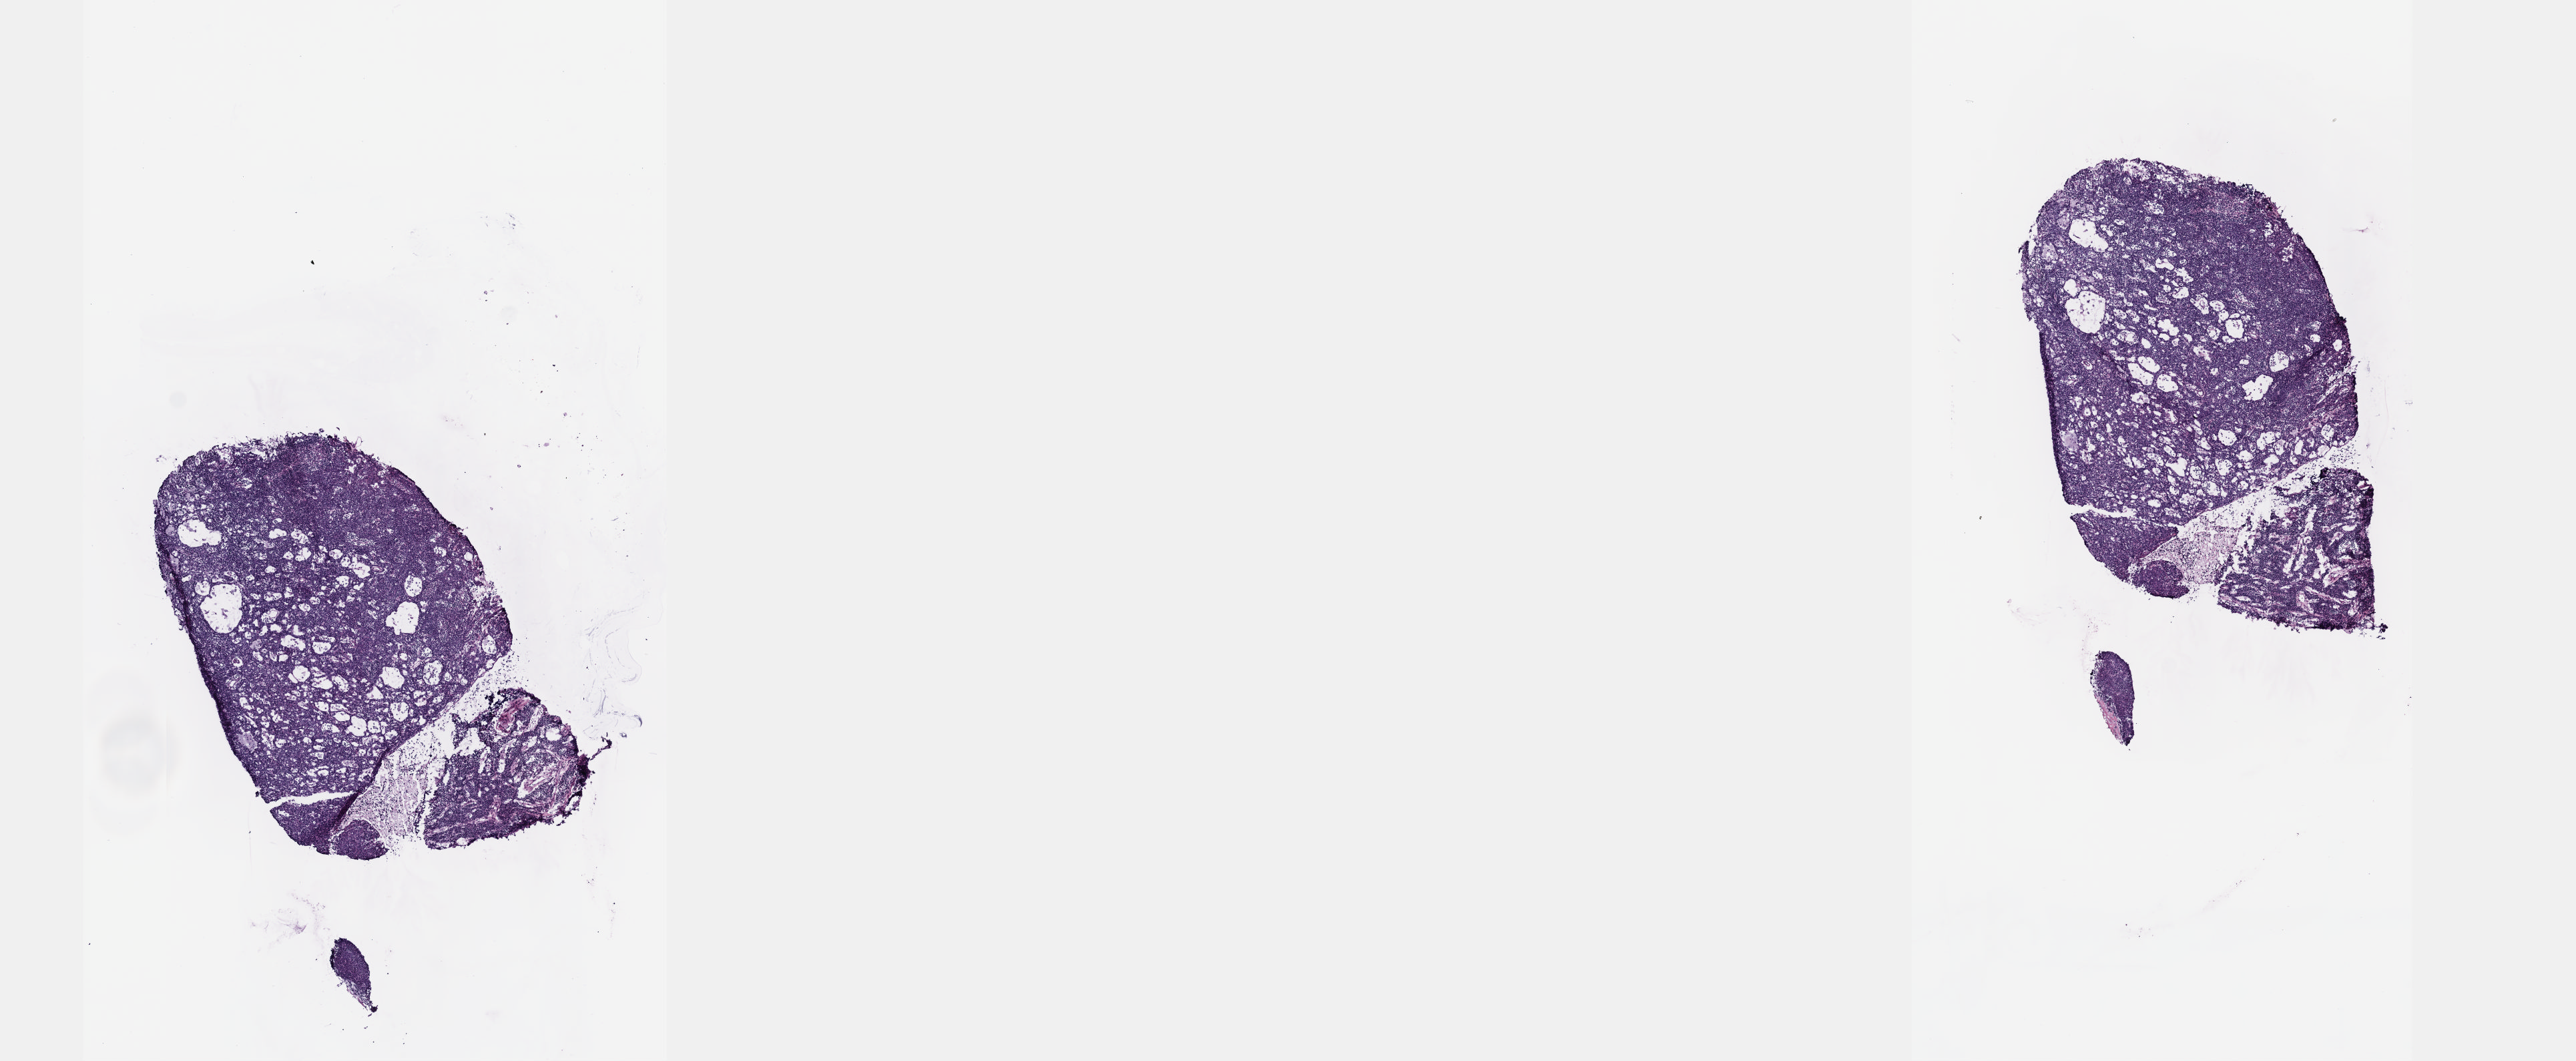
Digitized H&E-stained tissue section (whole slide) — low-resolution overview of the scanned area, about 15.6 x 6.4 mm (from a 40x scan). Frozen section from the top of the tissue portion. Sample: primary tumour, thymus. Patient: female, age at initial diagnosis 35 years. Composition of this section per pathologist review: tumour cells 99%, tumour nuclei 99%, normal cells 0%, stromal cells 1%, necrosis 0%. Inflammatory infiltration, as recorded: lymphocyte infiltration 0%, monocyte infiltration 0%, neutrophil infiltration 0%.
Pathologic diagnosis: Thymoma, type B2, malignant (anterior mediastinum).